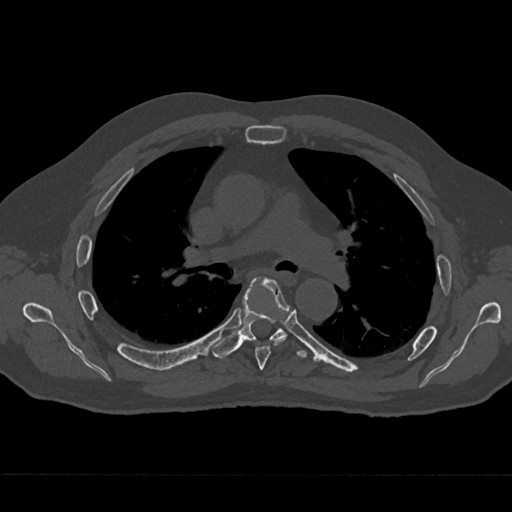
CT including the spine, one axial slice. Position 449 of 797 along the scan axis. Reconstruction kernel Br40s/3. 120 kVp. Bone window (W 1800 / L 400 HU). 0.5 mm slice thickness. 512 × 512 image matrix. Patient: male, 75 years. Case-level facts recorded for this patient, not image findings: primary cancer: renal; vertebrae with lytic lesions (as recorded): T4.
Annotated regions visible in this slice (semi-automatically segmented with operator editing):
- T5 vertebra: bounding box (x1, y1, x2, y2) in pixels: (255, 279, 290, 370)
- T6 vertebra: (211, 277, 307, 359)